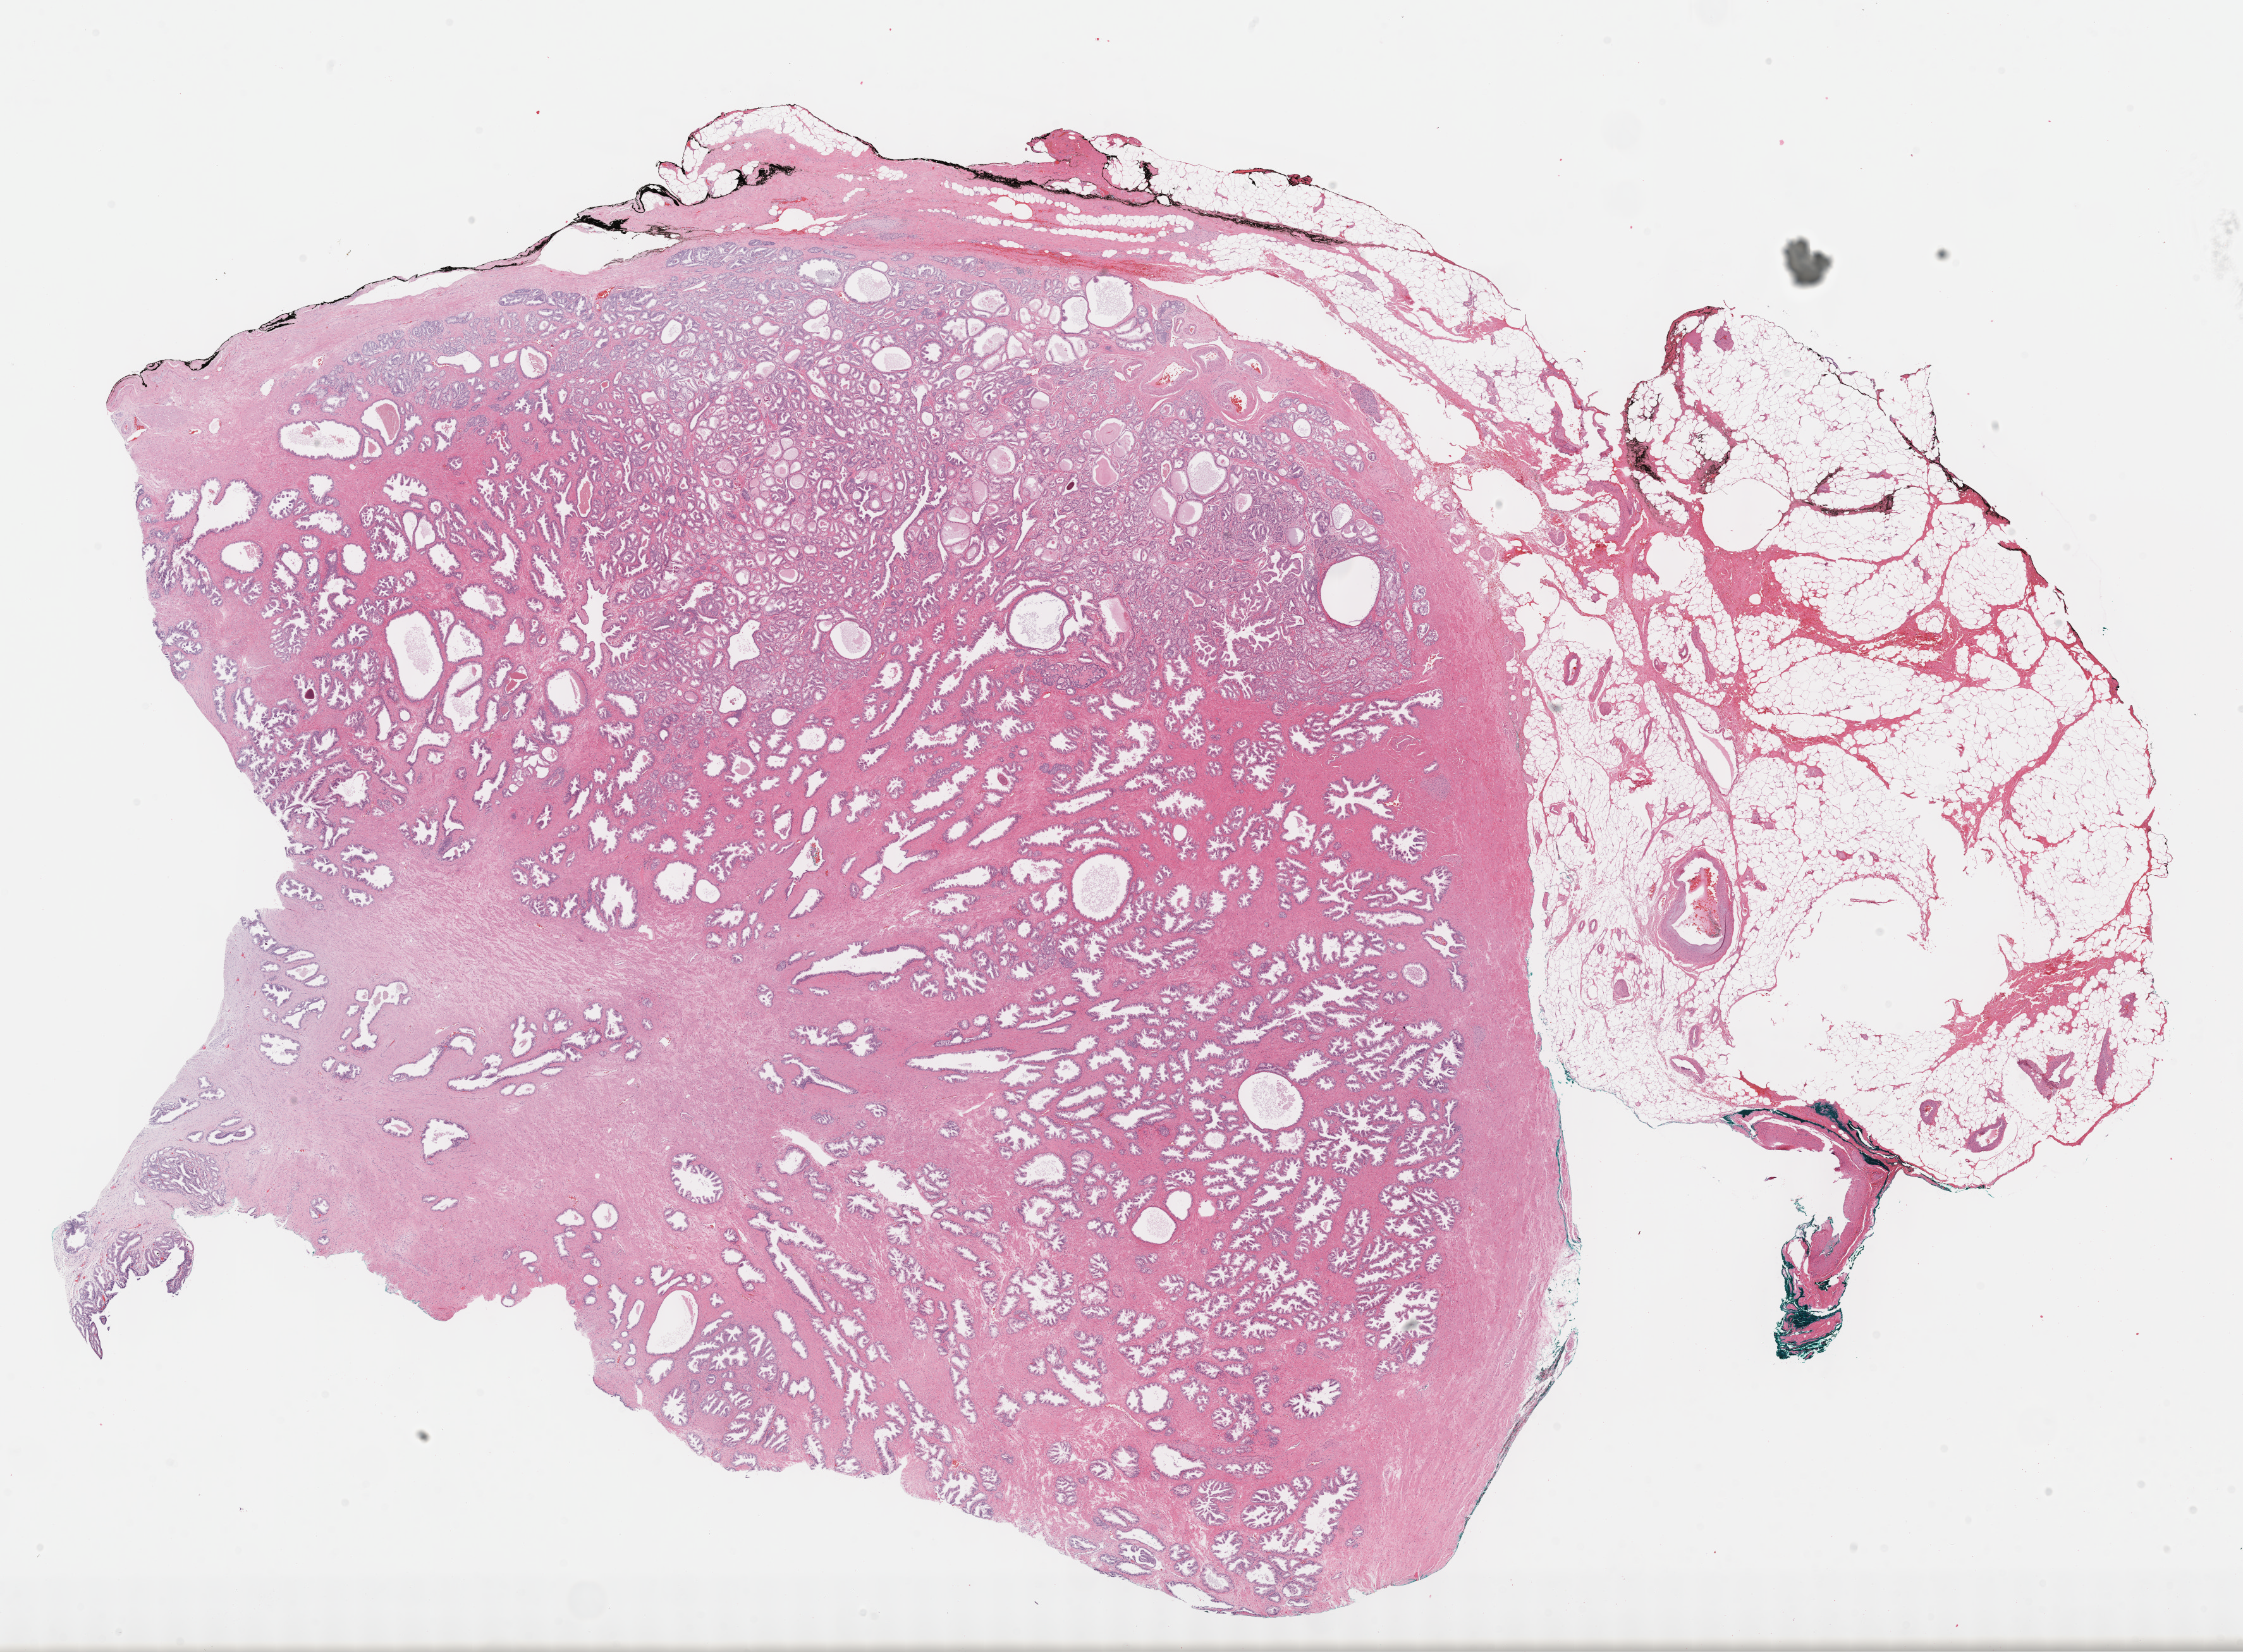
Hematoxylin and eosin (H&E) stained whole-slide image — shown as a low-resolution overview of the whole scanned area (about 28.7 x 21.1 mm, acquisition: 40x scan). Formalin-fixed paraffin-embedded (FFPE) diagnostic section. Sample: primary tumour, prostate. Patient: male, age at initial diagnosis 55 years. Gleason score: 7 (3+4).
- histologic diagnosis: Acinar cell carcinoma (prostate gland)